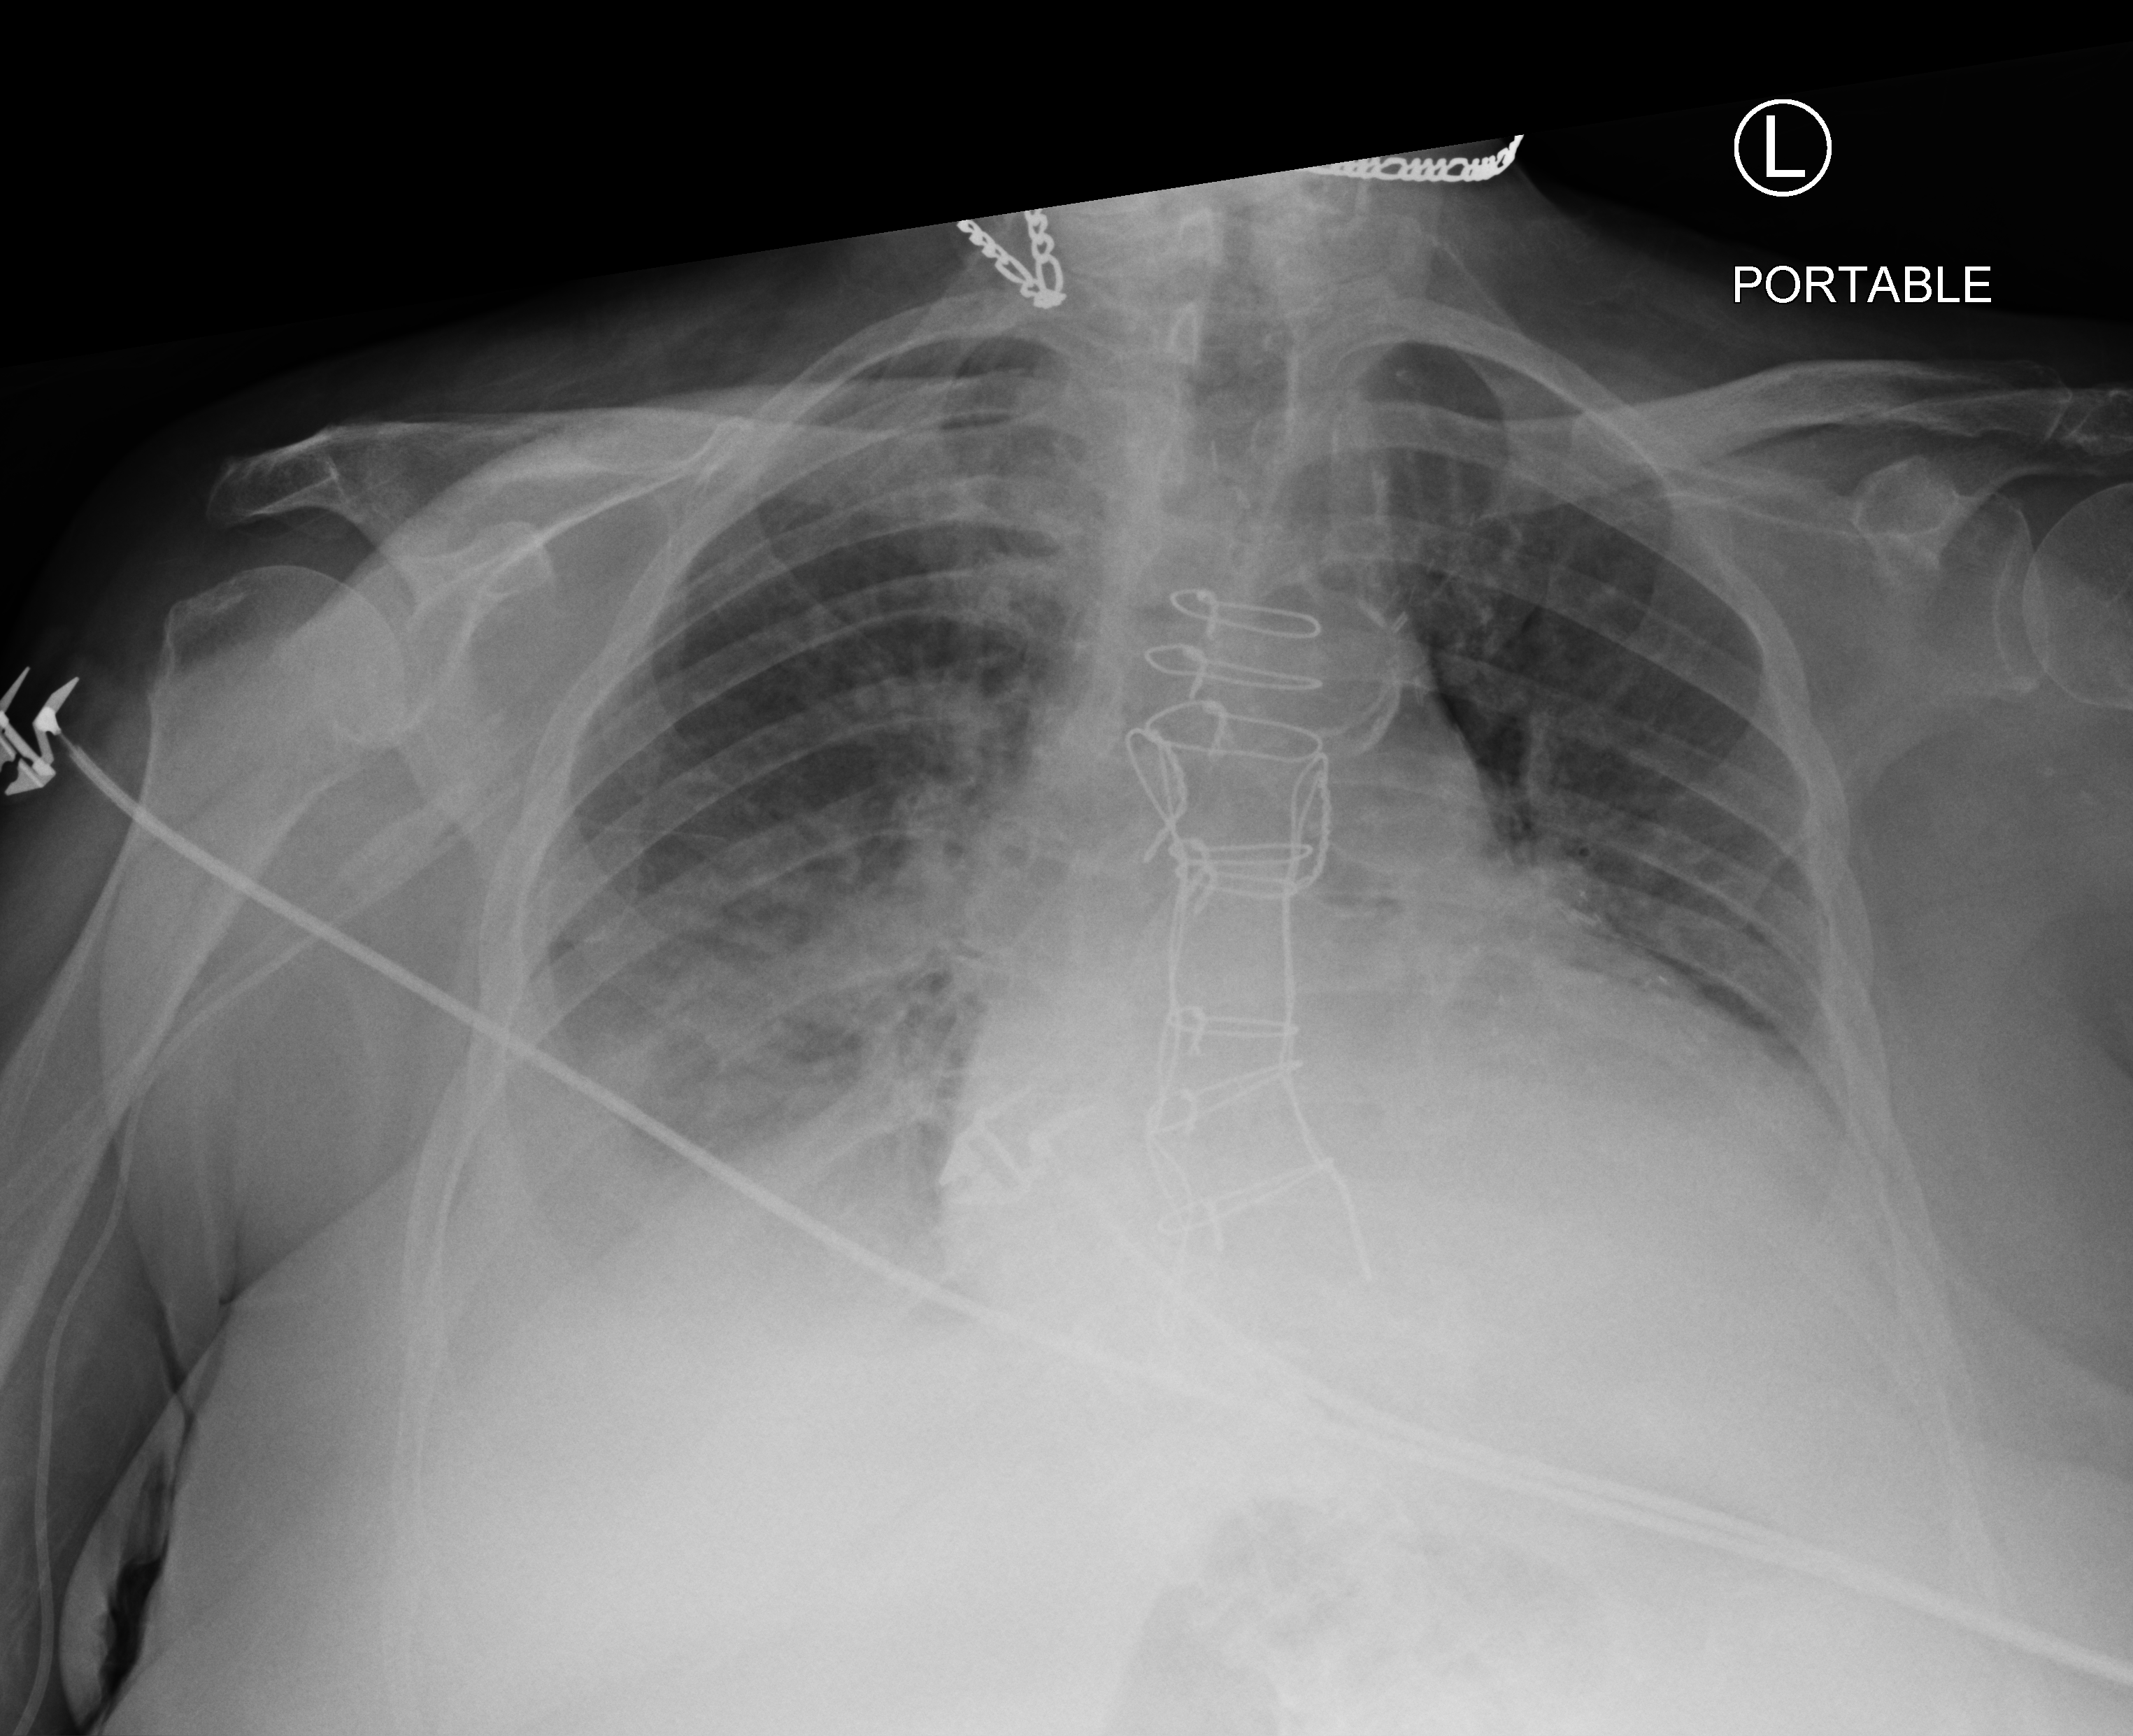
Portable chest radiograph, anteroposterior (AP) projection. Female patient hospitalised with COVID-19, age 75–90 years.
From the hospital-stay record, not from the radiograph (when in the stay this image was taken is not recorded): mechanically ventilated during this hospital stay: no.